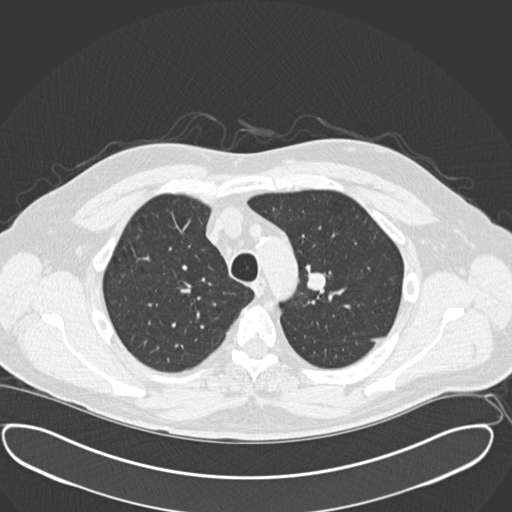
Axial slice from a low-dose chest CT screening exam, third annual screen, lung window (W 1500 / L -600 HU), 2 mm slice thickness, slice 44 of 181 in the series. Male, age 56 years at enrolment.
• Expert-annotated lung lesion, bounding box (x1, y1, x2, y2) in pixels: (289, 262, 343, 309).
• No non-calcified nodule or mass ≥4 mm was recorded by the screening reader at this exam.
• Official screen result: negative screen, minor abnormalities not suspicious for lung cancer.
• Participant outcome: lung cancer diagnosed 156 days after this screen — neuroendocrine carcinoma, NOS, left upper lobe, well differentiated (G1), stage IA (AJCC 6th edition), 20 mm at pathology.